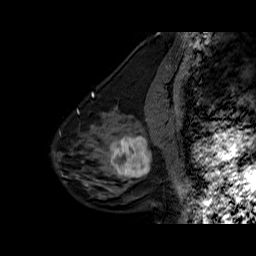
Breast MRI (dynamic contrast-enhanced), one sagittal slice. Slice 21 of 60 in the series (ordered by position). Dynamic contrast-enhanced series, time point 2 of 6 at this slice position (early post-contrast). 1.5 T. TE 6.3 ms, TR 32.5 ms. 256 × 256 image matrix, field of view 200 × 200 mm. Female patient. Case-level facts recorded for this patient, not image findings: setting: breast cancer imaged before/during neoadjuvant chemotherapy; receptor status: triple-negative.
Annotated regions visible in this slice (semi-automatic segmentation, software-assisted and operator-edited):
- analysis volume of interest (the breast-tissue region the enhancement analysis was run in; not a lesion): bounding box <102,127,162,186> (left, top, right, bottom; pixels)
- tumour enhancement mask (voxels above the 100 % enhancement threshold inside the analysis volume of interest): <110,136,151,177>